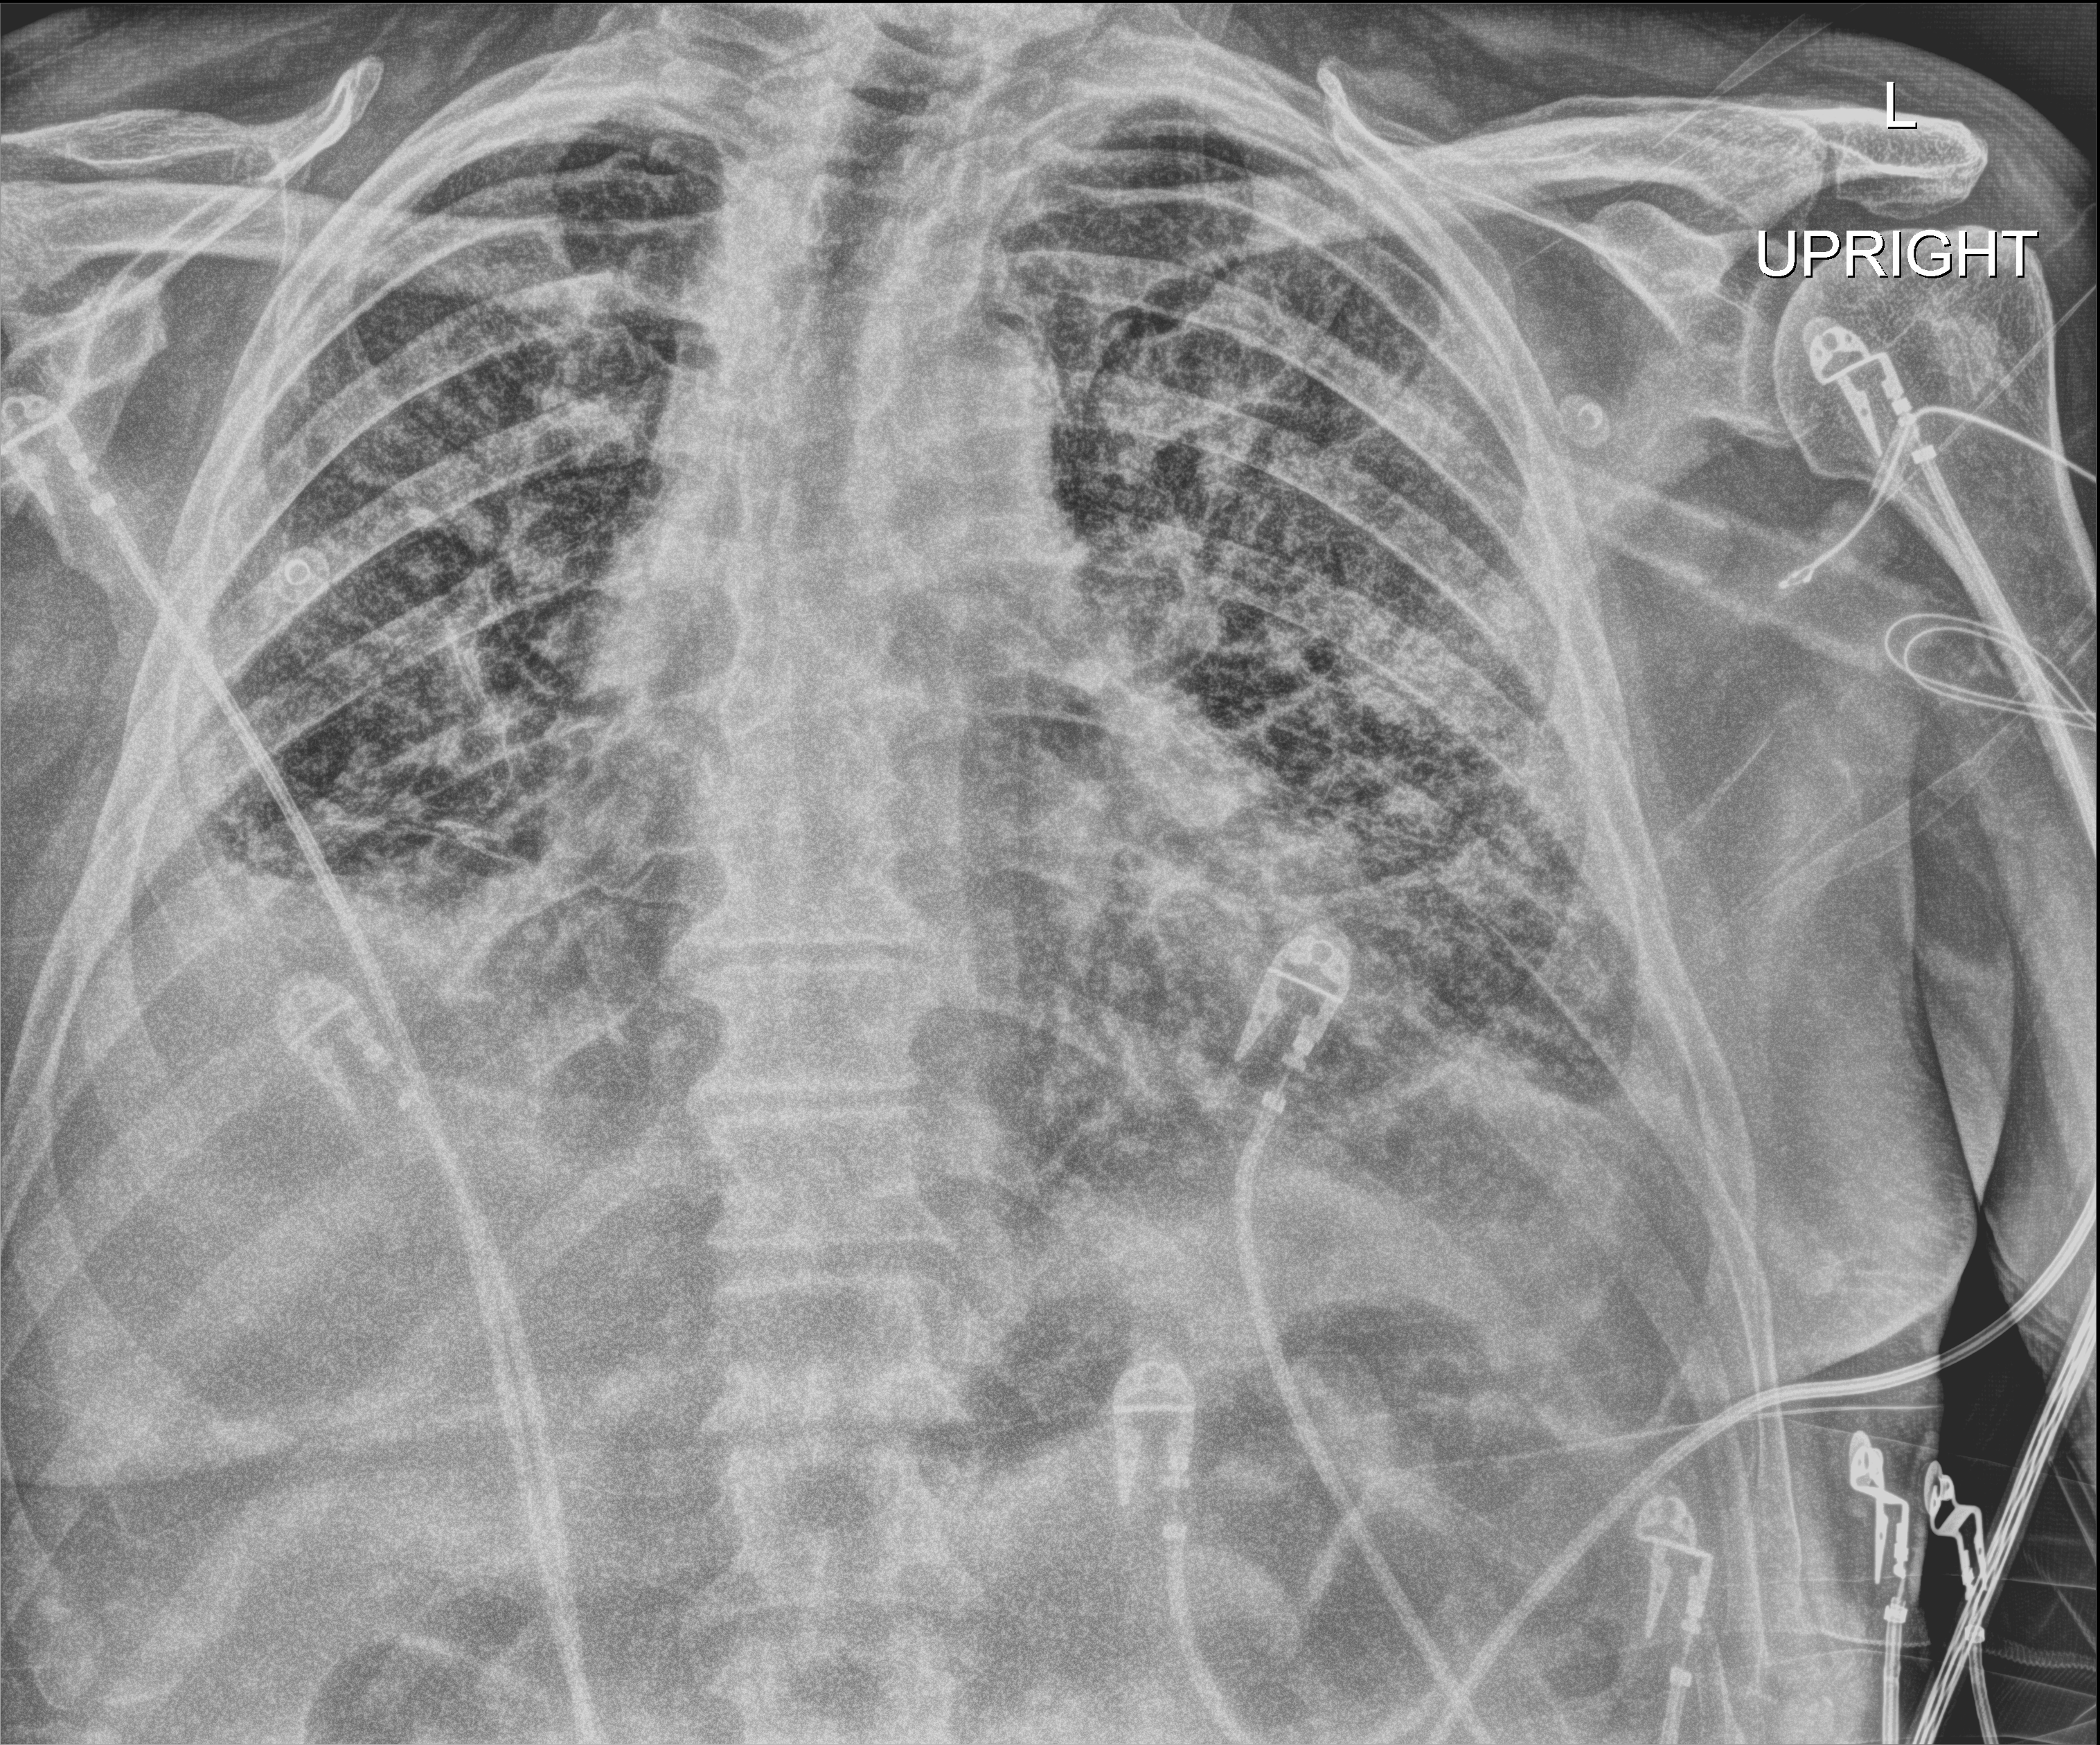
Chest X-ray (portable), anteroposterior (AP) projection. Male patient hospitalised with COVID-19, age 75–90 years.
Admission-level facts for this patient (not findings on this image; timing relative to this image not recorded):
- admitted to intensive care during this hospital stay: yes